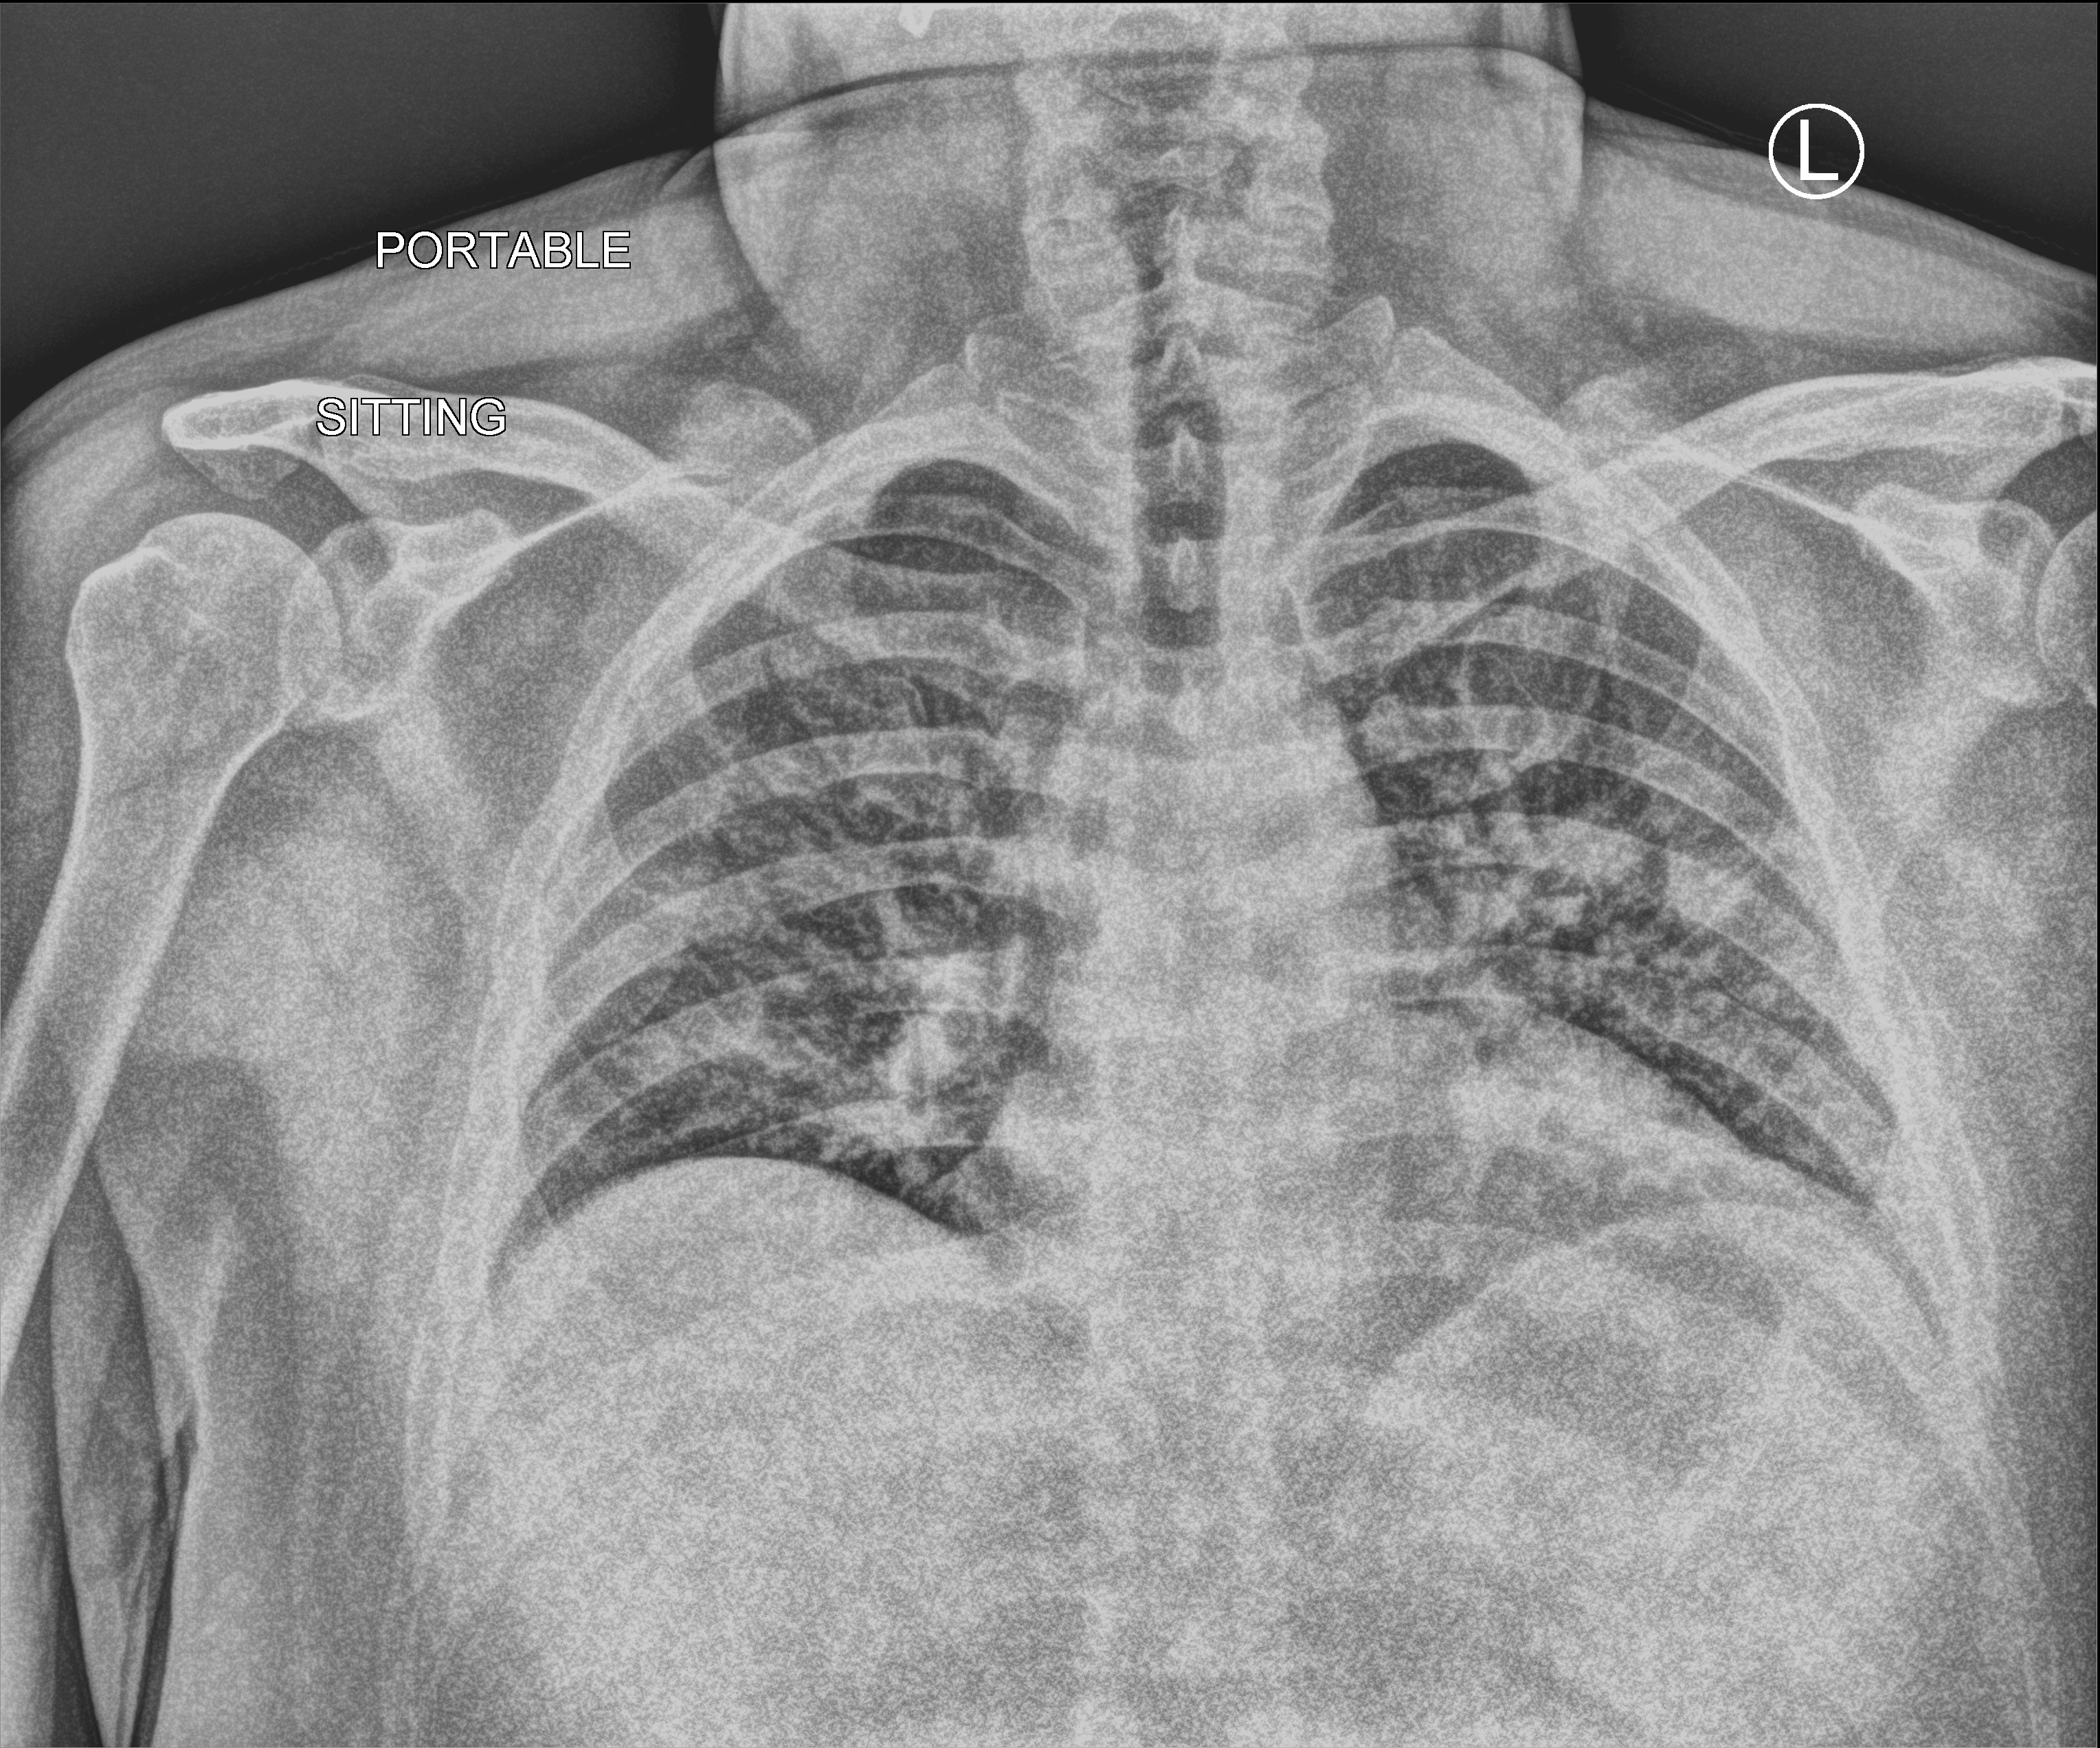
Portable chest radiograph; anteroposterior (AP) projection. Male patient hospitalised with COVID-19, age 18–59 years.
From the hospital-stay record, not from the radiograph (when in the stay this image was taken is not recorded):
- mechanically ventilated during this hospital stay: yes
- chronic kidney disease (admission record): no
- admitted to intensive care during this hospital stay: yes